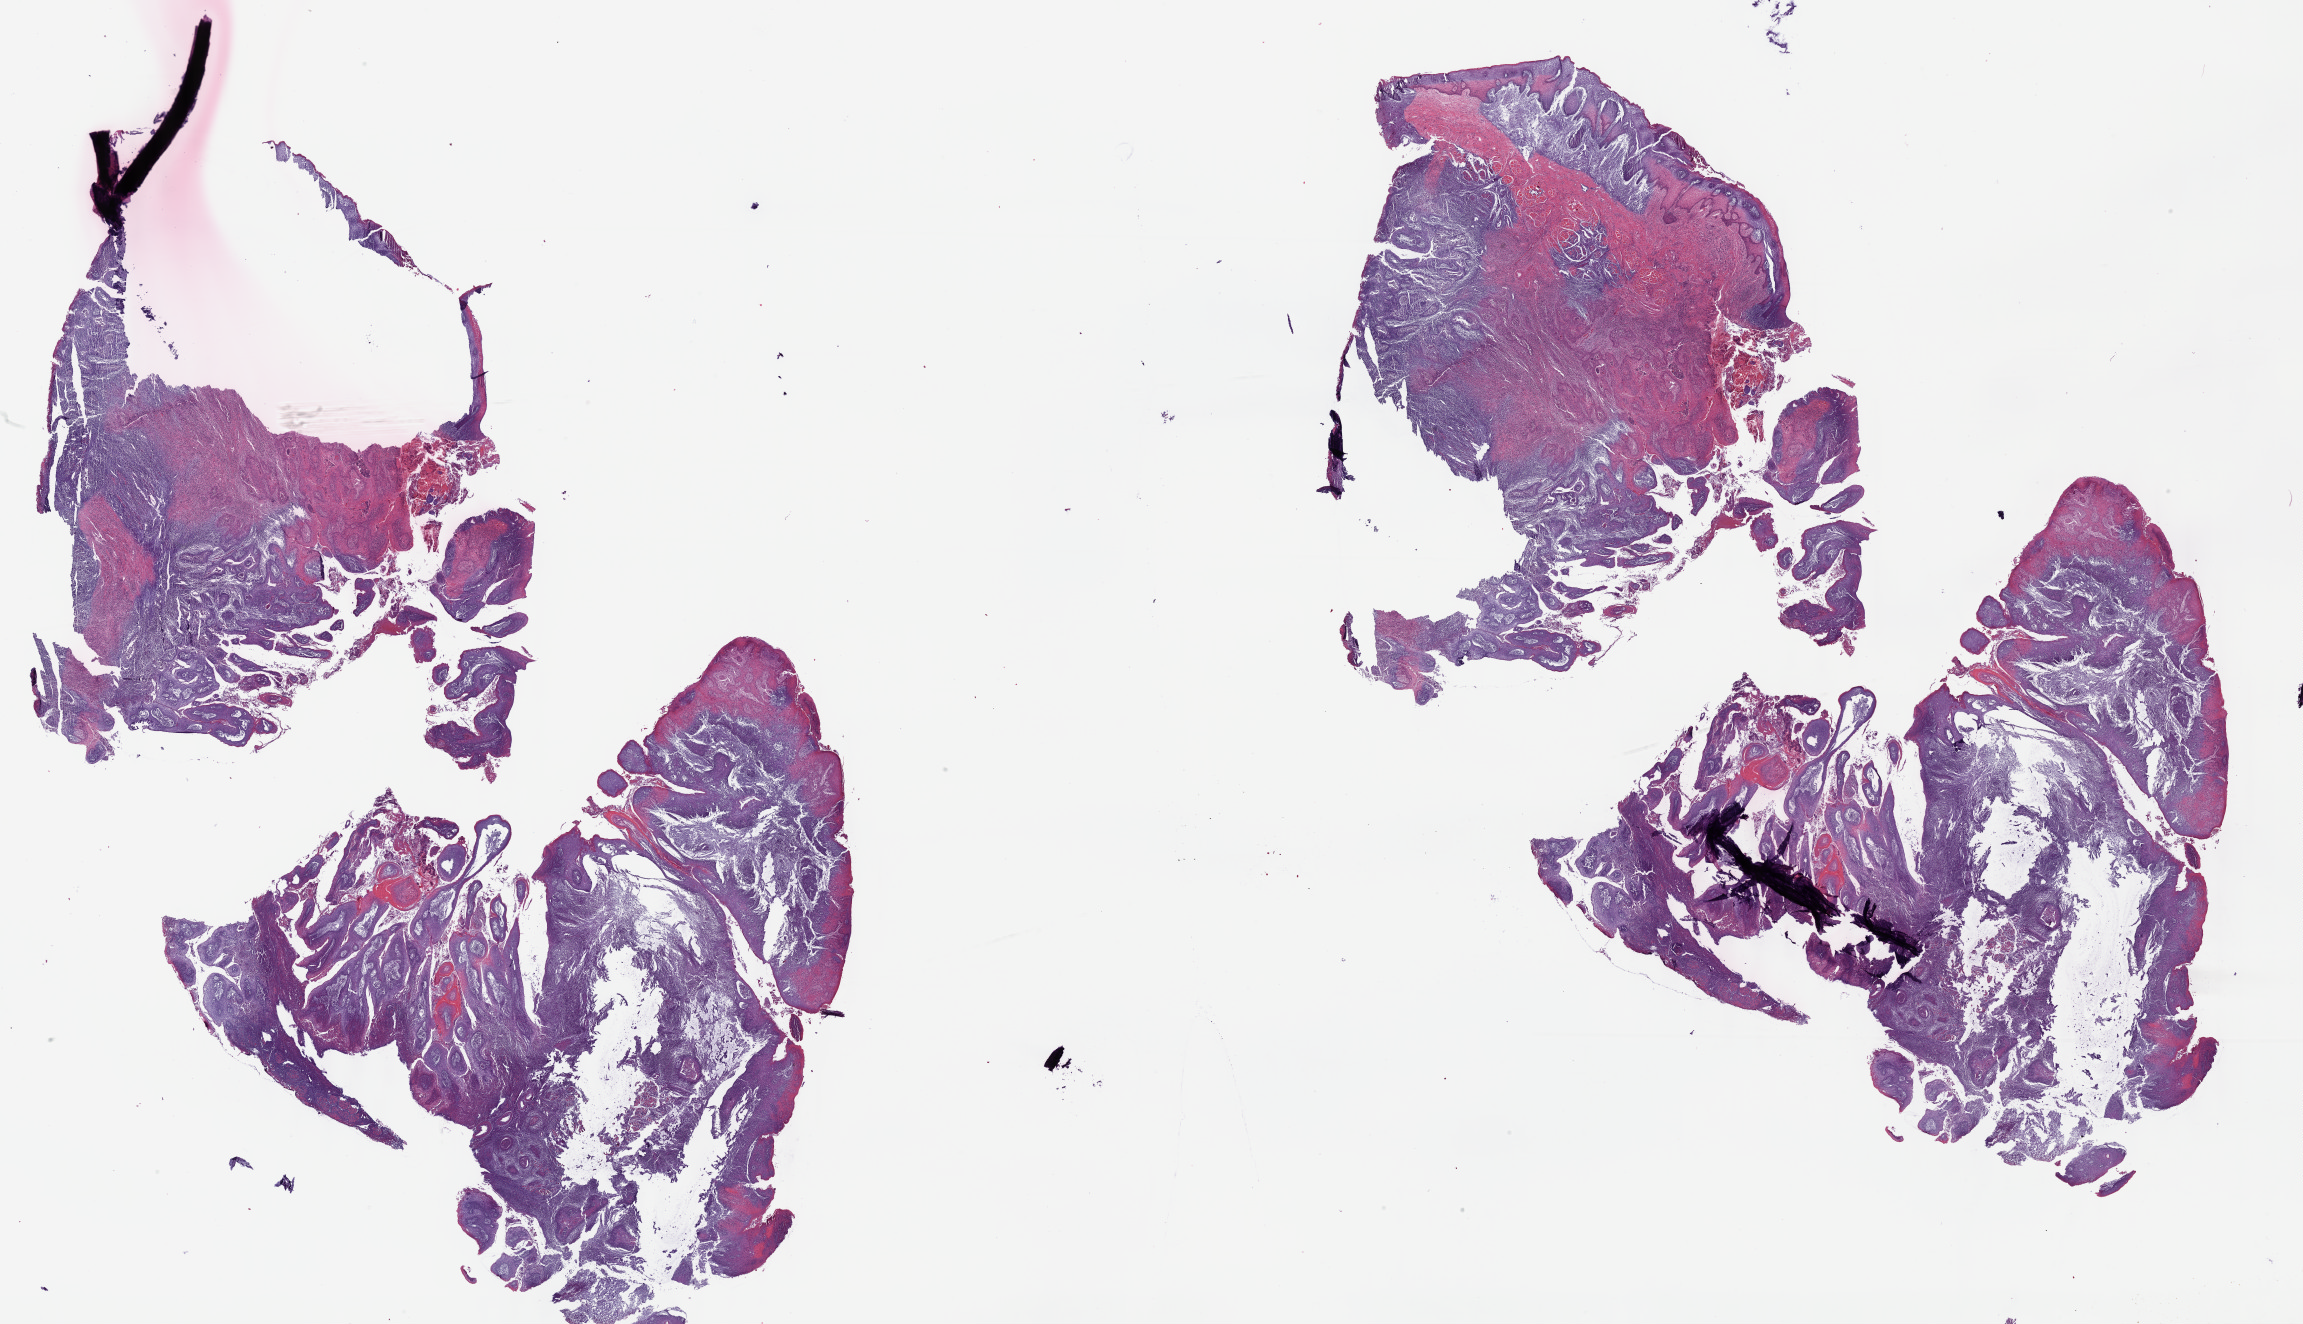
Hematoxylin and eosin (H&E) stained whole-slide image, shown as a low-resolution overview of the whole scanned area (about 37.2 x 21.4 mm, from a 40x scan); formalin-fixed paraffin-embedded (FFPE) diagnostic section; primary tumour sample from the head and neck. Female, age 82 years at initial diagnosis. Histologic grade: G2 (moderately differentiated).
• AJCC pathologic stage: I (5th edition)
• histologic diagnosis: Squamous cell carcinoma, NOS (tongue, NOS)